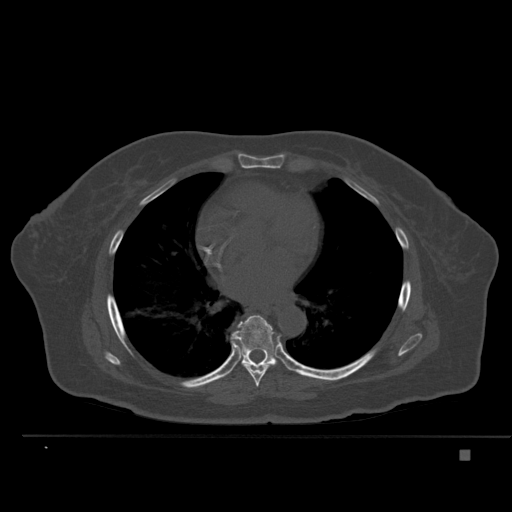
CT including the spine, one axial slice; slice 318 of 477 in the series (ordered by position); bone window (W 1800 / L 400 HU); 1.5 mm slice thickness; 512 × 512 image matrix, field of view 422 × 422 mm. Female patient, age 74 years. Case-level facts recorded for this patient, not image findings: primary cancer: colon.
Structures marked on this image (semi-automatic segmentation, software-assisted and operator-edited):
- T7 vertebra: bounding box [x1, y1, x2, y2] px = [232, 339, 272, 387]
- T8 vertebra: [231, 315, 277, 370]